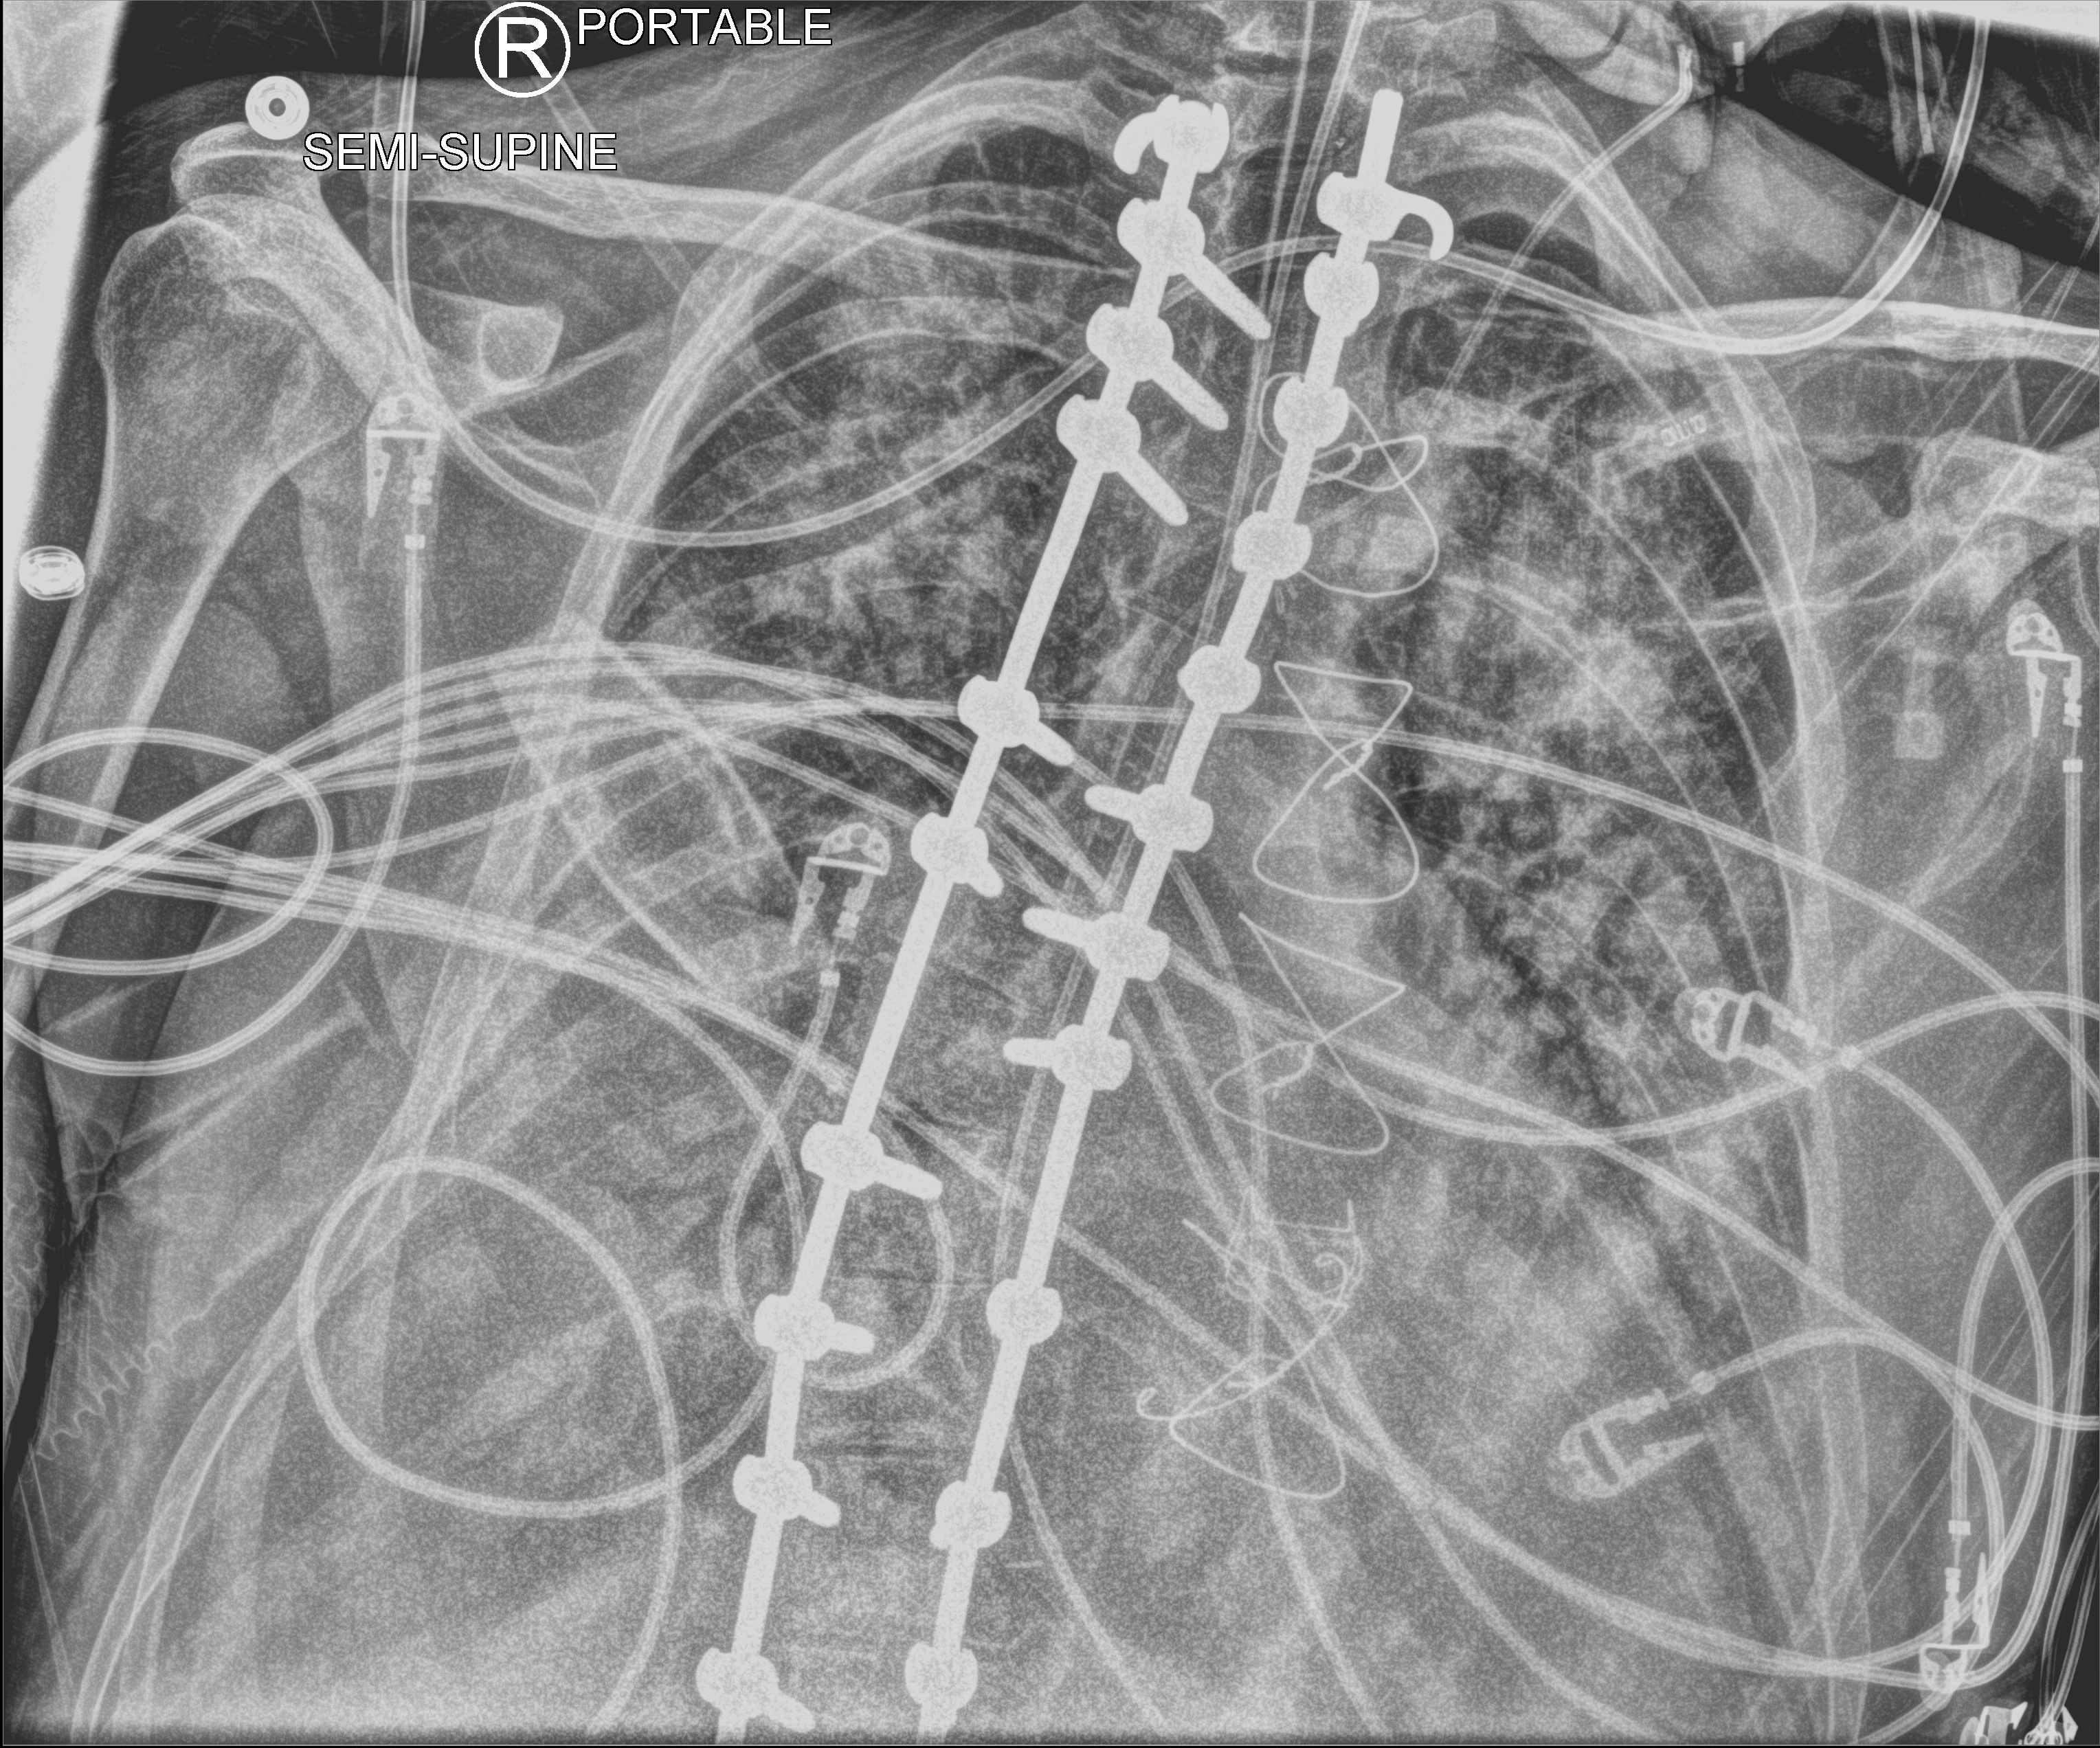
Portable chest radiograph, anteroposterior (AP) projection. Adult patient hospitalised with COVID-19, age 18–59 years.
From the hospital-stay record, not from the radiograph (when in the stay this image was taken is not recorded):
- COPD (admission record): no
- mechanically ventilated during this hospital stay: yes
- admitted to intensive care during this hospital stay: yes